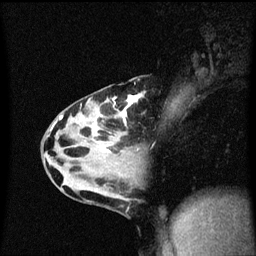
Breast MRI (dynamic contrast-enhanced), one sagittal slice. Position 27 of 60 along the scan axis. Dynamic contrast-enhanced series, image 2 of 3 at this slice position (ordered by acquisition). 1.5 T. TE 4.2 ms, TR 8.4 ms. 256 × 256 image matrix, field of view 200 × 200 mm. Patient: female, 32 years.
Annotated regions visible in this slice (semi-automatically segmented with operator editing):
- analysis volume of interest (the breast-tissue region the enhancement analysis was run in; not a lesion): bounding box [x1, y1, x2, y2] px = [55, 78, 177, 167]
- tumour enhancement mask (voxels above the 70 % enhancement threshold inside the analysis volume of interest): [60, 94, 143, 153]